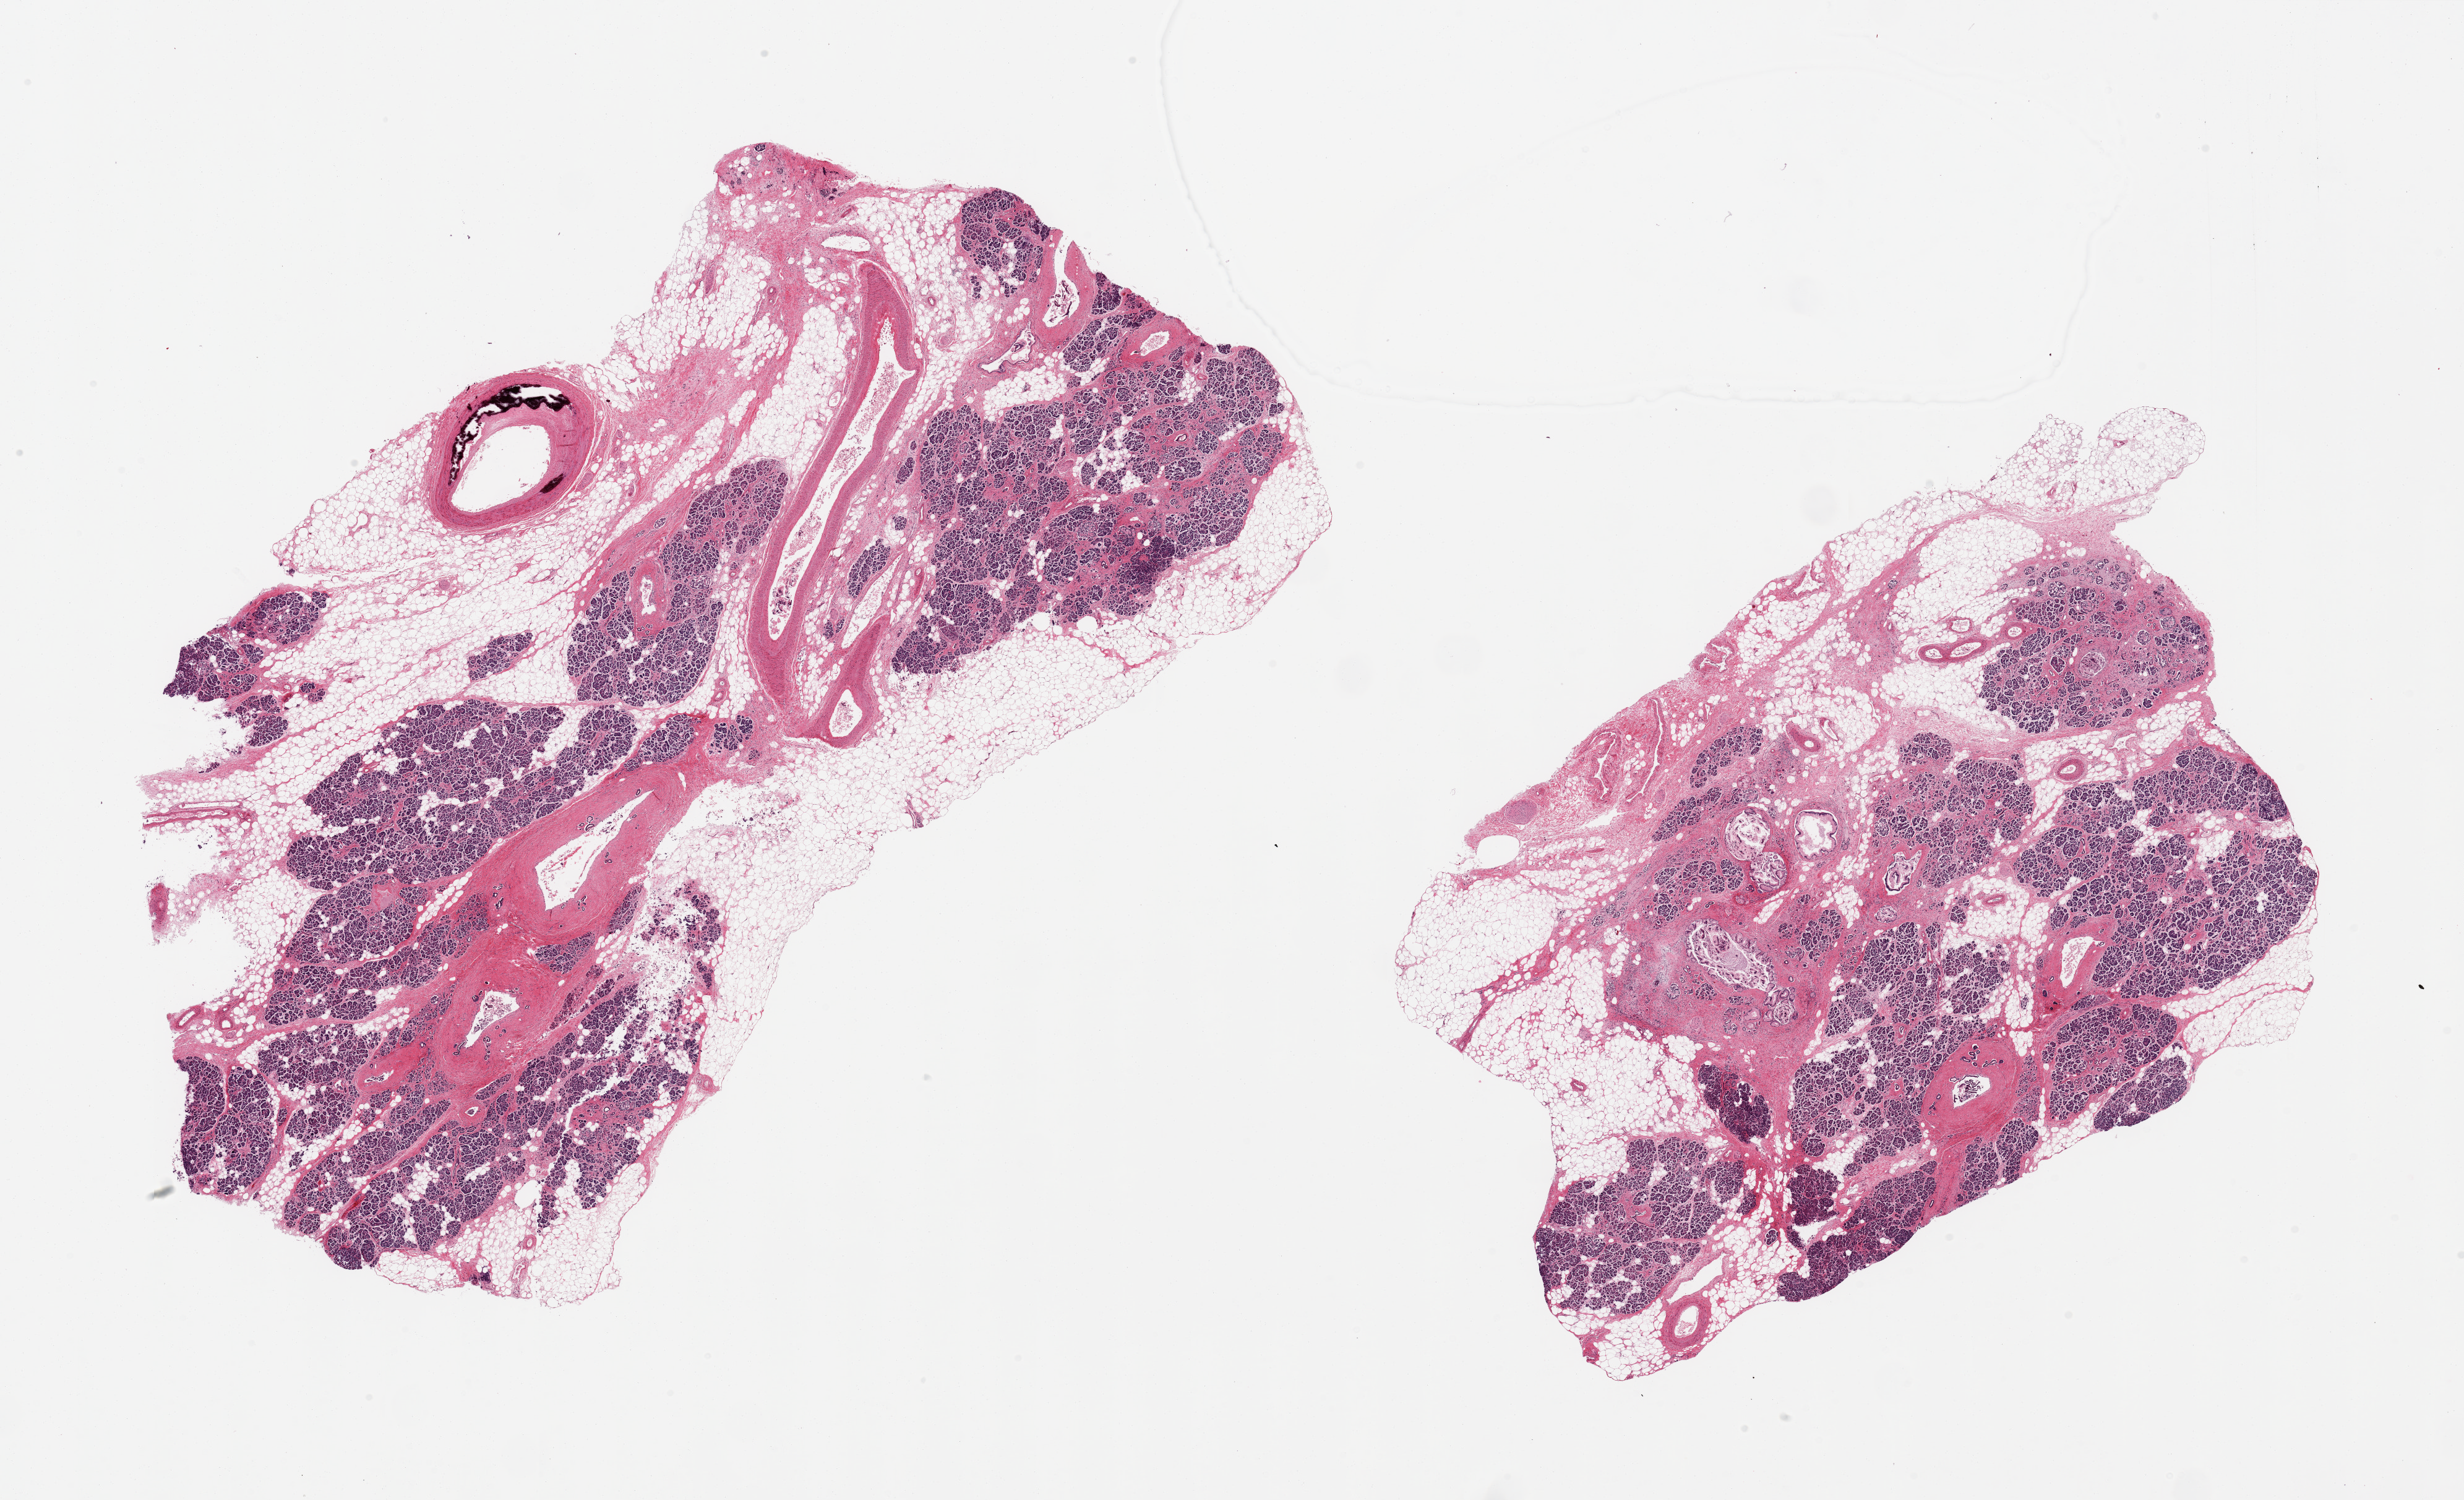
Whole-slide image, hematoxylin and eosin (H&E) stain, brightfield — low-resolution overview of the scanned area, about 31.5 x 19.2 mm (acquisition: 20x scan); PAXgene-fixed, paraffin-embedded tissue; section of pancreas (target tissue); donor tissue sample.
Reviewer comment on this tissue sample: 2 pieces, ~50% interstitial fat, moderate-advance saponification, Islets not preserved. Evidence of remote fibrosing pancreatitis.